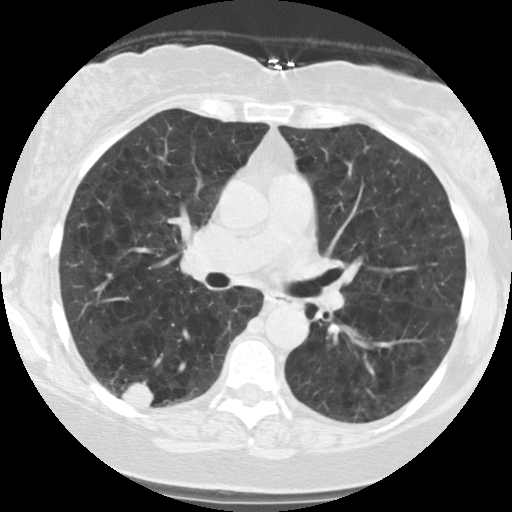
Low-dose screening chest CT, one axial slice. Slice 66 of 122 in the series (ordered by position). Lung window (W 1500 / L -600 HU). 512 × 512 image matrix.
Annotated regions visible in this slice (manually delineated by an expert):
- lesion 1 (tumor, lower lobe of right lung): bounding box (x1, y1, x2, y2) in pixels: (121, 381, 154, 408)